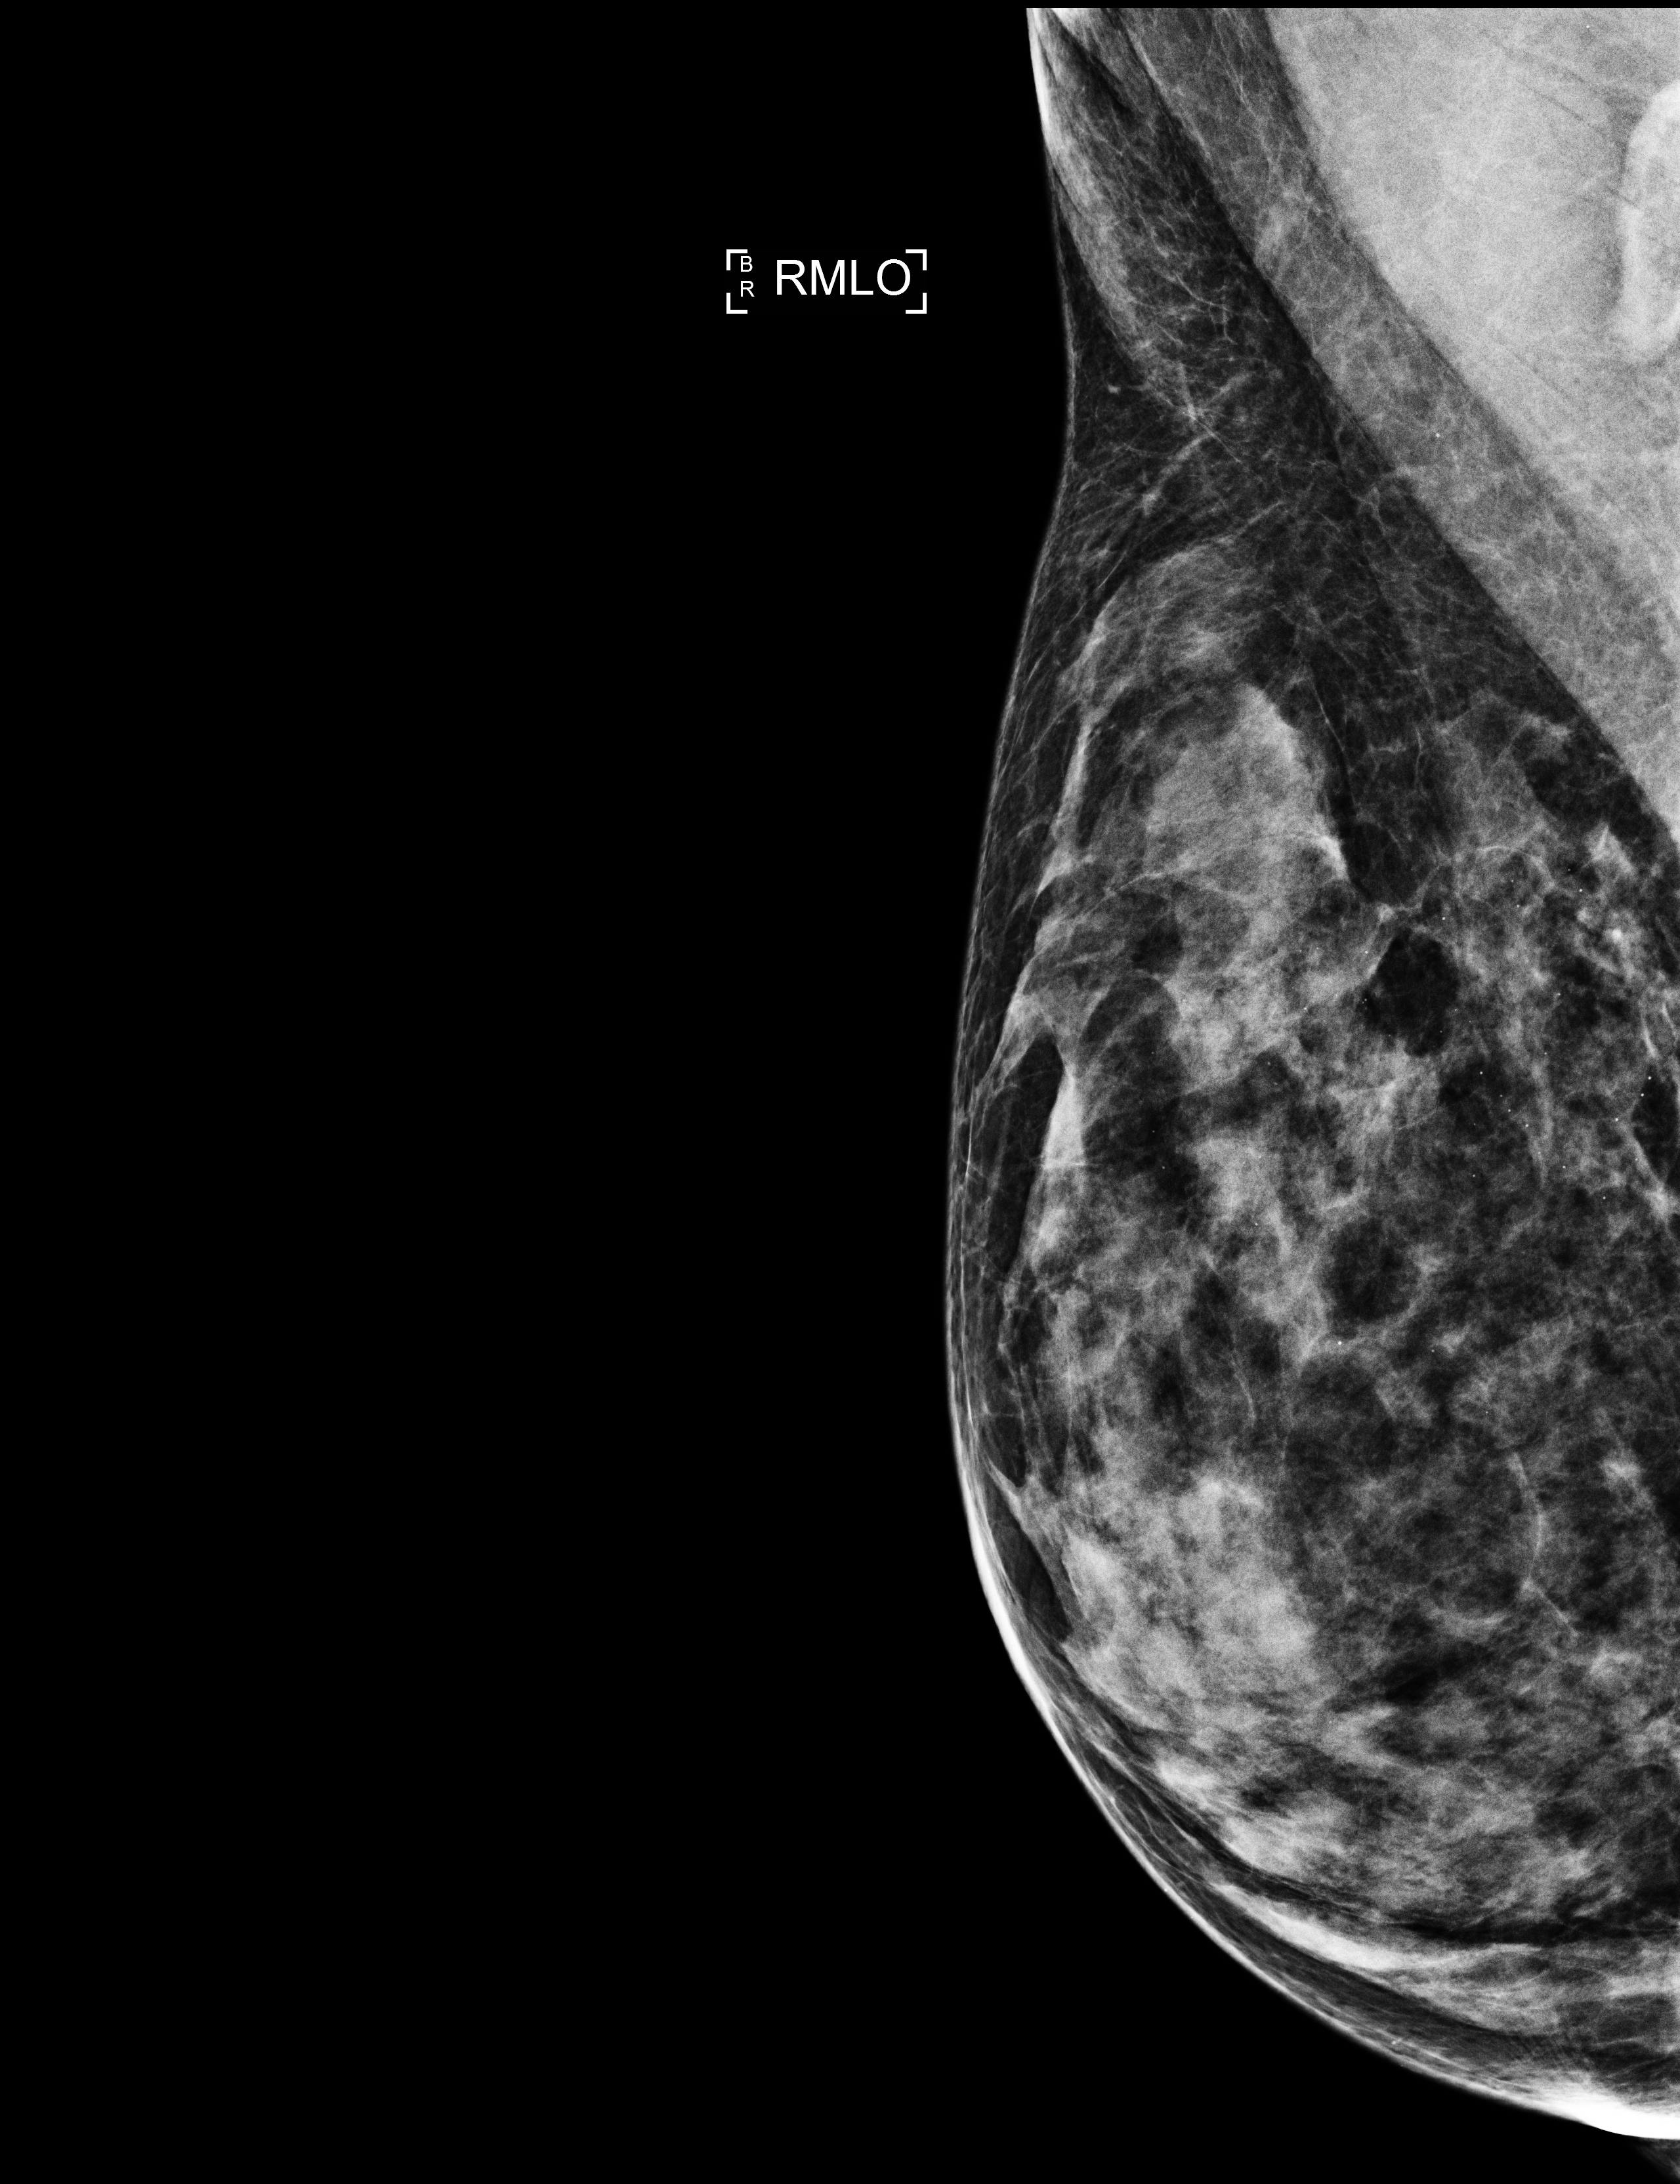
Screening examination, compressed breast thickness 46 mm, system: Selenia Dimensions. Patient: female, 47 years.
Image type: full-field digital mammogram. Breast: right. Projection: MLO view.